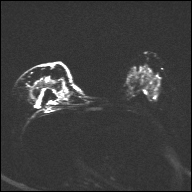
Breast MRI, one axial slice. Position 19 of 32 along the scan axis. Diffusion-weighted series; image 2 of 4 stored at this slice position (different b-values; order by instance number). 1.5 T. 192 × 192 image matrix. Female patient.
Structures marked on this image (outlined manually by an expert reader):
- tumour on diffusion-weighted imaging: box from (x=39, y=80) to (x=56, y=87) px